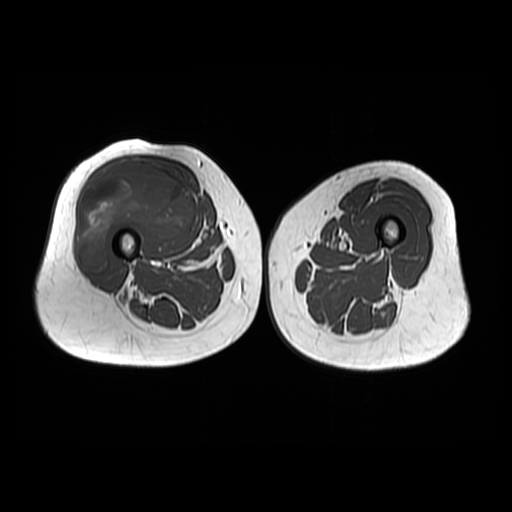
MRI of an extremity soft-tissue mass, one axial slice; slice 25 of 48 in the series (ordered by position); 6 mm slice thickness; 512 × 512 image matrix, field of view 440 × 440 mm. Female patient. Case-level facts recorded for this patient, not image findings: histological type: pleiomorphic undifferentiated sarcoma; grade: high; site of the primary tumour: right quadricep.
Structures marked on this image (outlined manually by an expert reader):
- gross tumour volume including surrounding oedema: box from (x=78, y=158) to (x=194, y=272) px
- gross tumour volume (mass): (x=78, y=158)–(x=194, y=272)